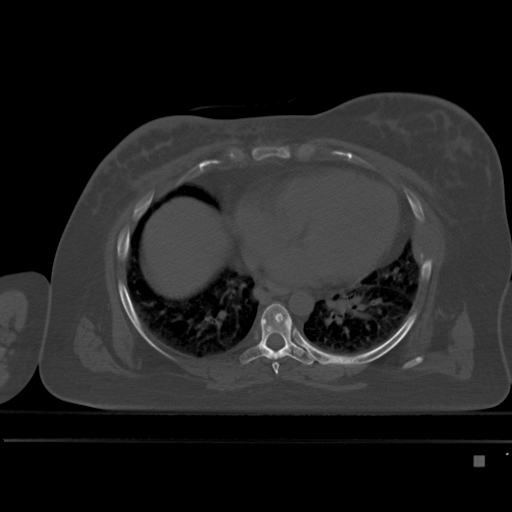
CT including the spine, one axial slice. Slice 294 of 495 in the series (ordered by position). Bone window (W 1800 / L 400 HU). 1.5 mm slice thickness. 512 × 512 image matrix. Female patient, age 33 years. Case-level facts recorded for this patient, not image findings: primary cancer: breast; vertebrae with lytic lesions (as recorded): T1.
Structures marked on this image (semi-automatically segmented with operator editing):
- T6 vertebra: bounding box [x1, y1, x2, y2] px = [272, 362, 279, 374]
- T7 vertebra: [240, 303, 315, 365]